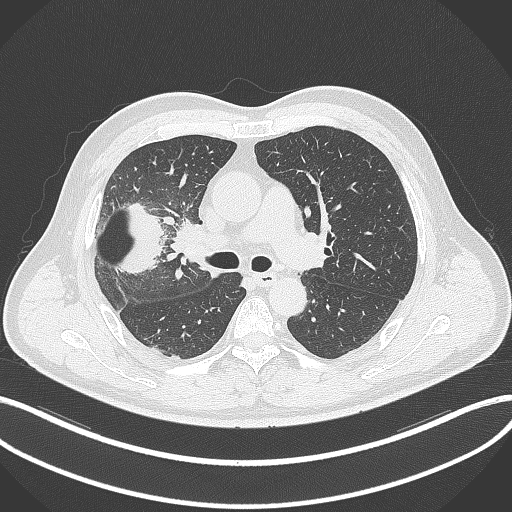
Chest CT, one axial slice. Position 205 of 348 along the scan axis. Lung window (W 1500 / L -600 HU). 1 mm slice thickness. 512 × 512 image matrix. Patient: male, 55 years. From the clinical record (not read from this slice): clinical TNM (as recorded): T3 N2 M1.
Outlined on this slice (rectangle marked by the reading radiologist):
- lung tumour (recorded histology: adenocarcinoma): bounding box <112,191,172,275> (left, top, right, bottom; pixels)